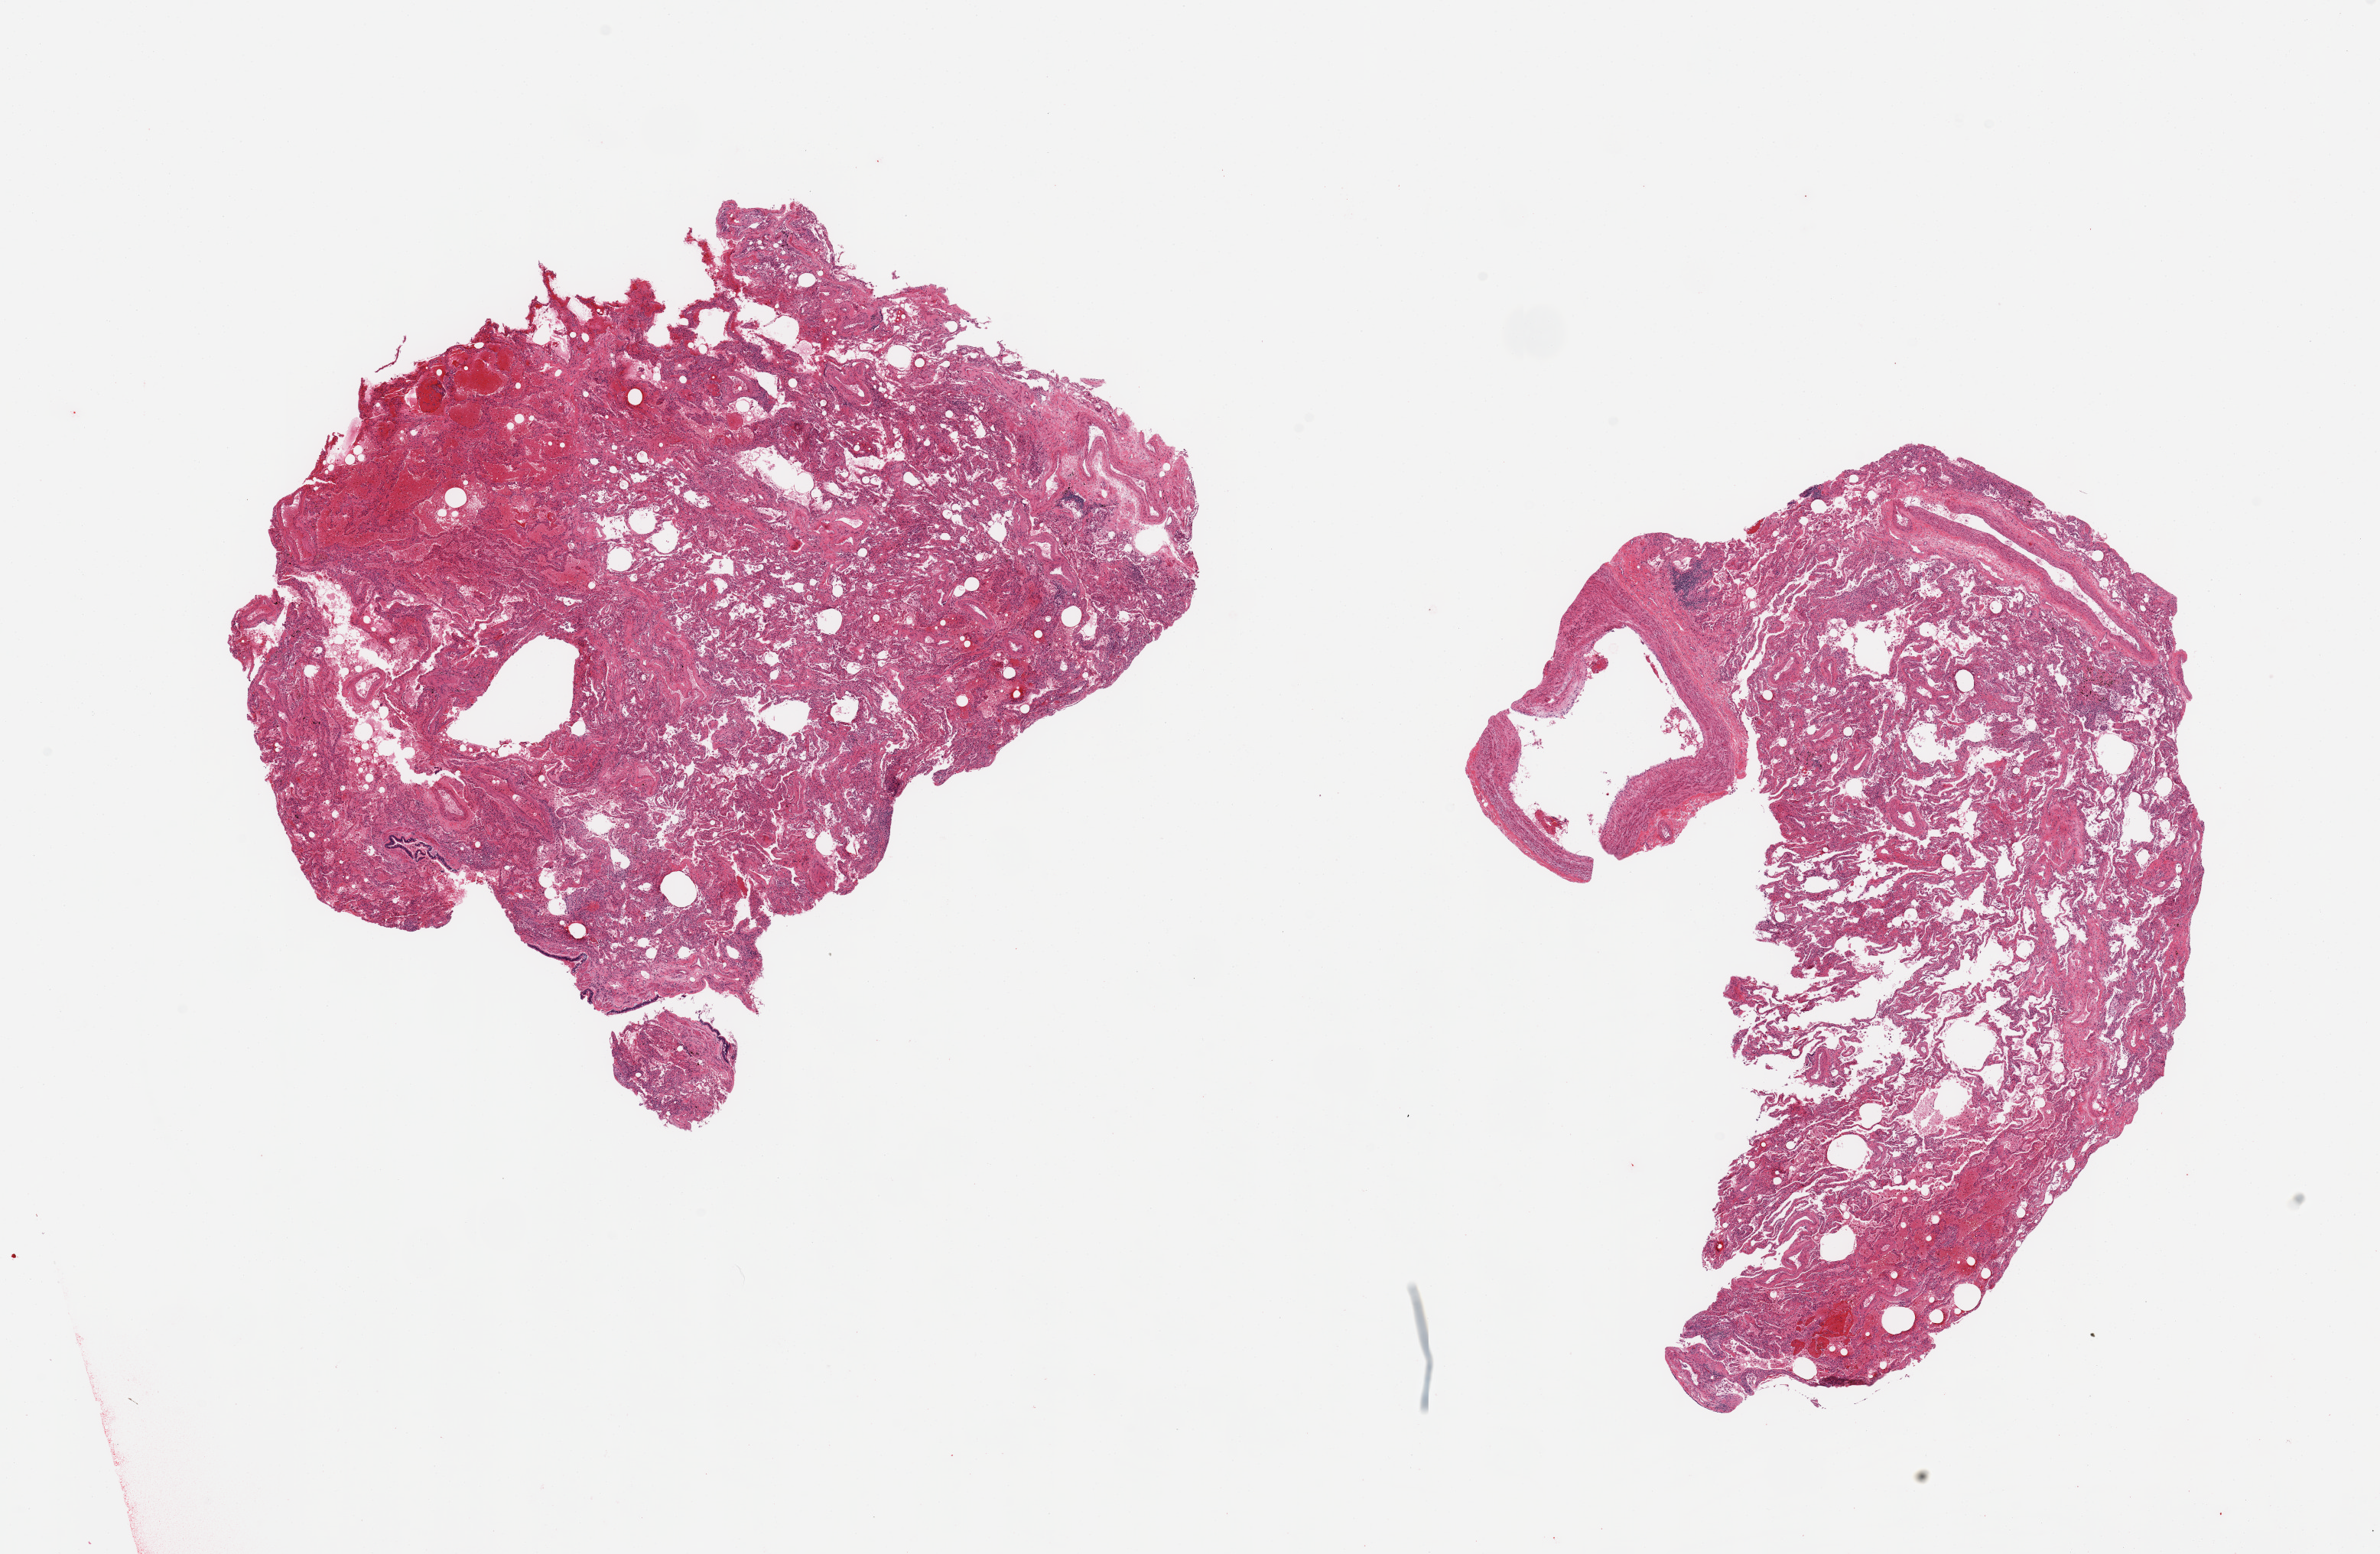
Whole-slide image, H&E stain — whole scanned area (about 24.6 x 16.1 mm, slide scanned at 20x) shown as a low-resolution overview. PAXgene-fixed paraffin-embedded (PFPE) section. Target tissue: lung. Donor tissue sample. Donor sex: male.
Review note (as recorded): 2 piece; moderate interstitial fibrosis; 3mm focus of alveolar hemorrhage.